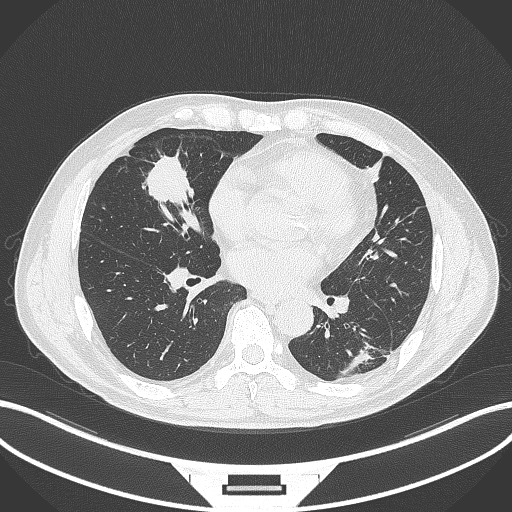
Chest CT, one axial slice. Slice 129 of 399 in the series (ordered by position). Reconstruction kernel B70f. Lung window (W 1500 / L -600 HU). 1 mm slice thickness. 512 × 512 image matrix, field of view 400 × 400 mm. Patient: male, 59 years. From the clinical record (not read from this slice): clinical TNM (as recorded): T2a N1 M0.
Outlined on this slice (rectangle marked by the reading radiologist):
- lung tumour (recorded histology: adenocarcinoma): box from (x=143, y=153) to (x=197, y=207) px